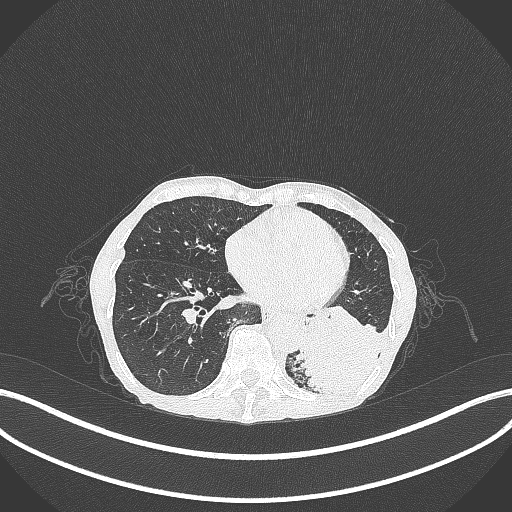
Chest CT, one axial slice; slice 90 of 347 in the series (ordered by position); reconstruction kernel B70f; 120 kVp; lung window (W 1500 / L -600 HU); 512 × 512 image matrix. Female patient, age 70 years. Case-level facts recorded for this patient, not image findings: clinical TNM (as recorded): T3 N0 M0; histopathological grade: G3.
Outlined on this slice (bounding box drawn by a radiologist):
- lung tumour (recorded histology: small cell carcinoma): bounding box [x1, y1, x2, y2] px = [296, 311, 384, 396]